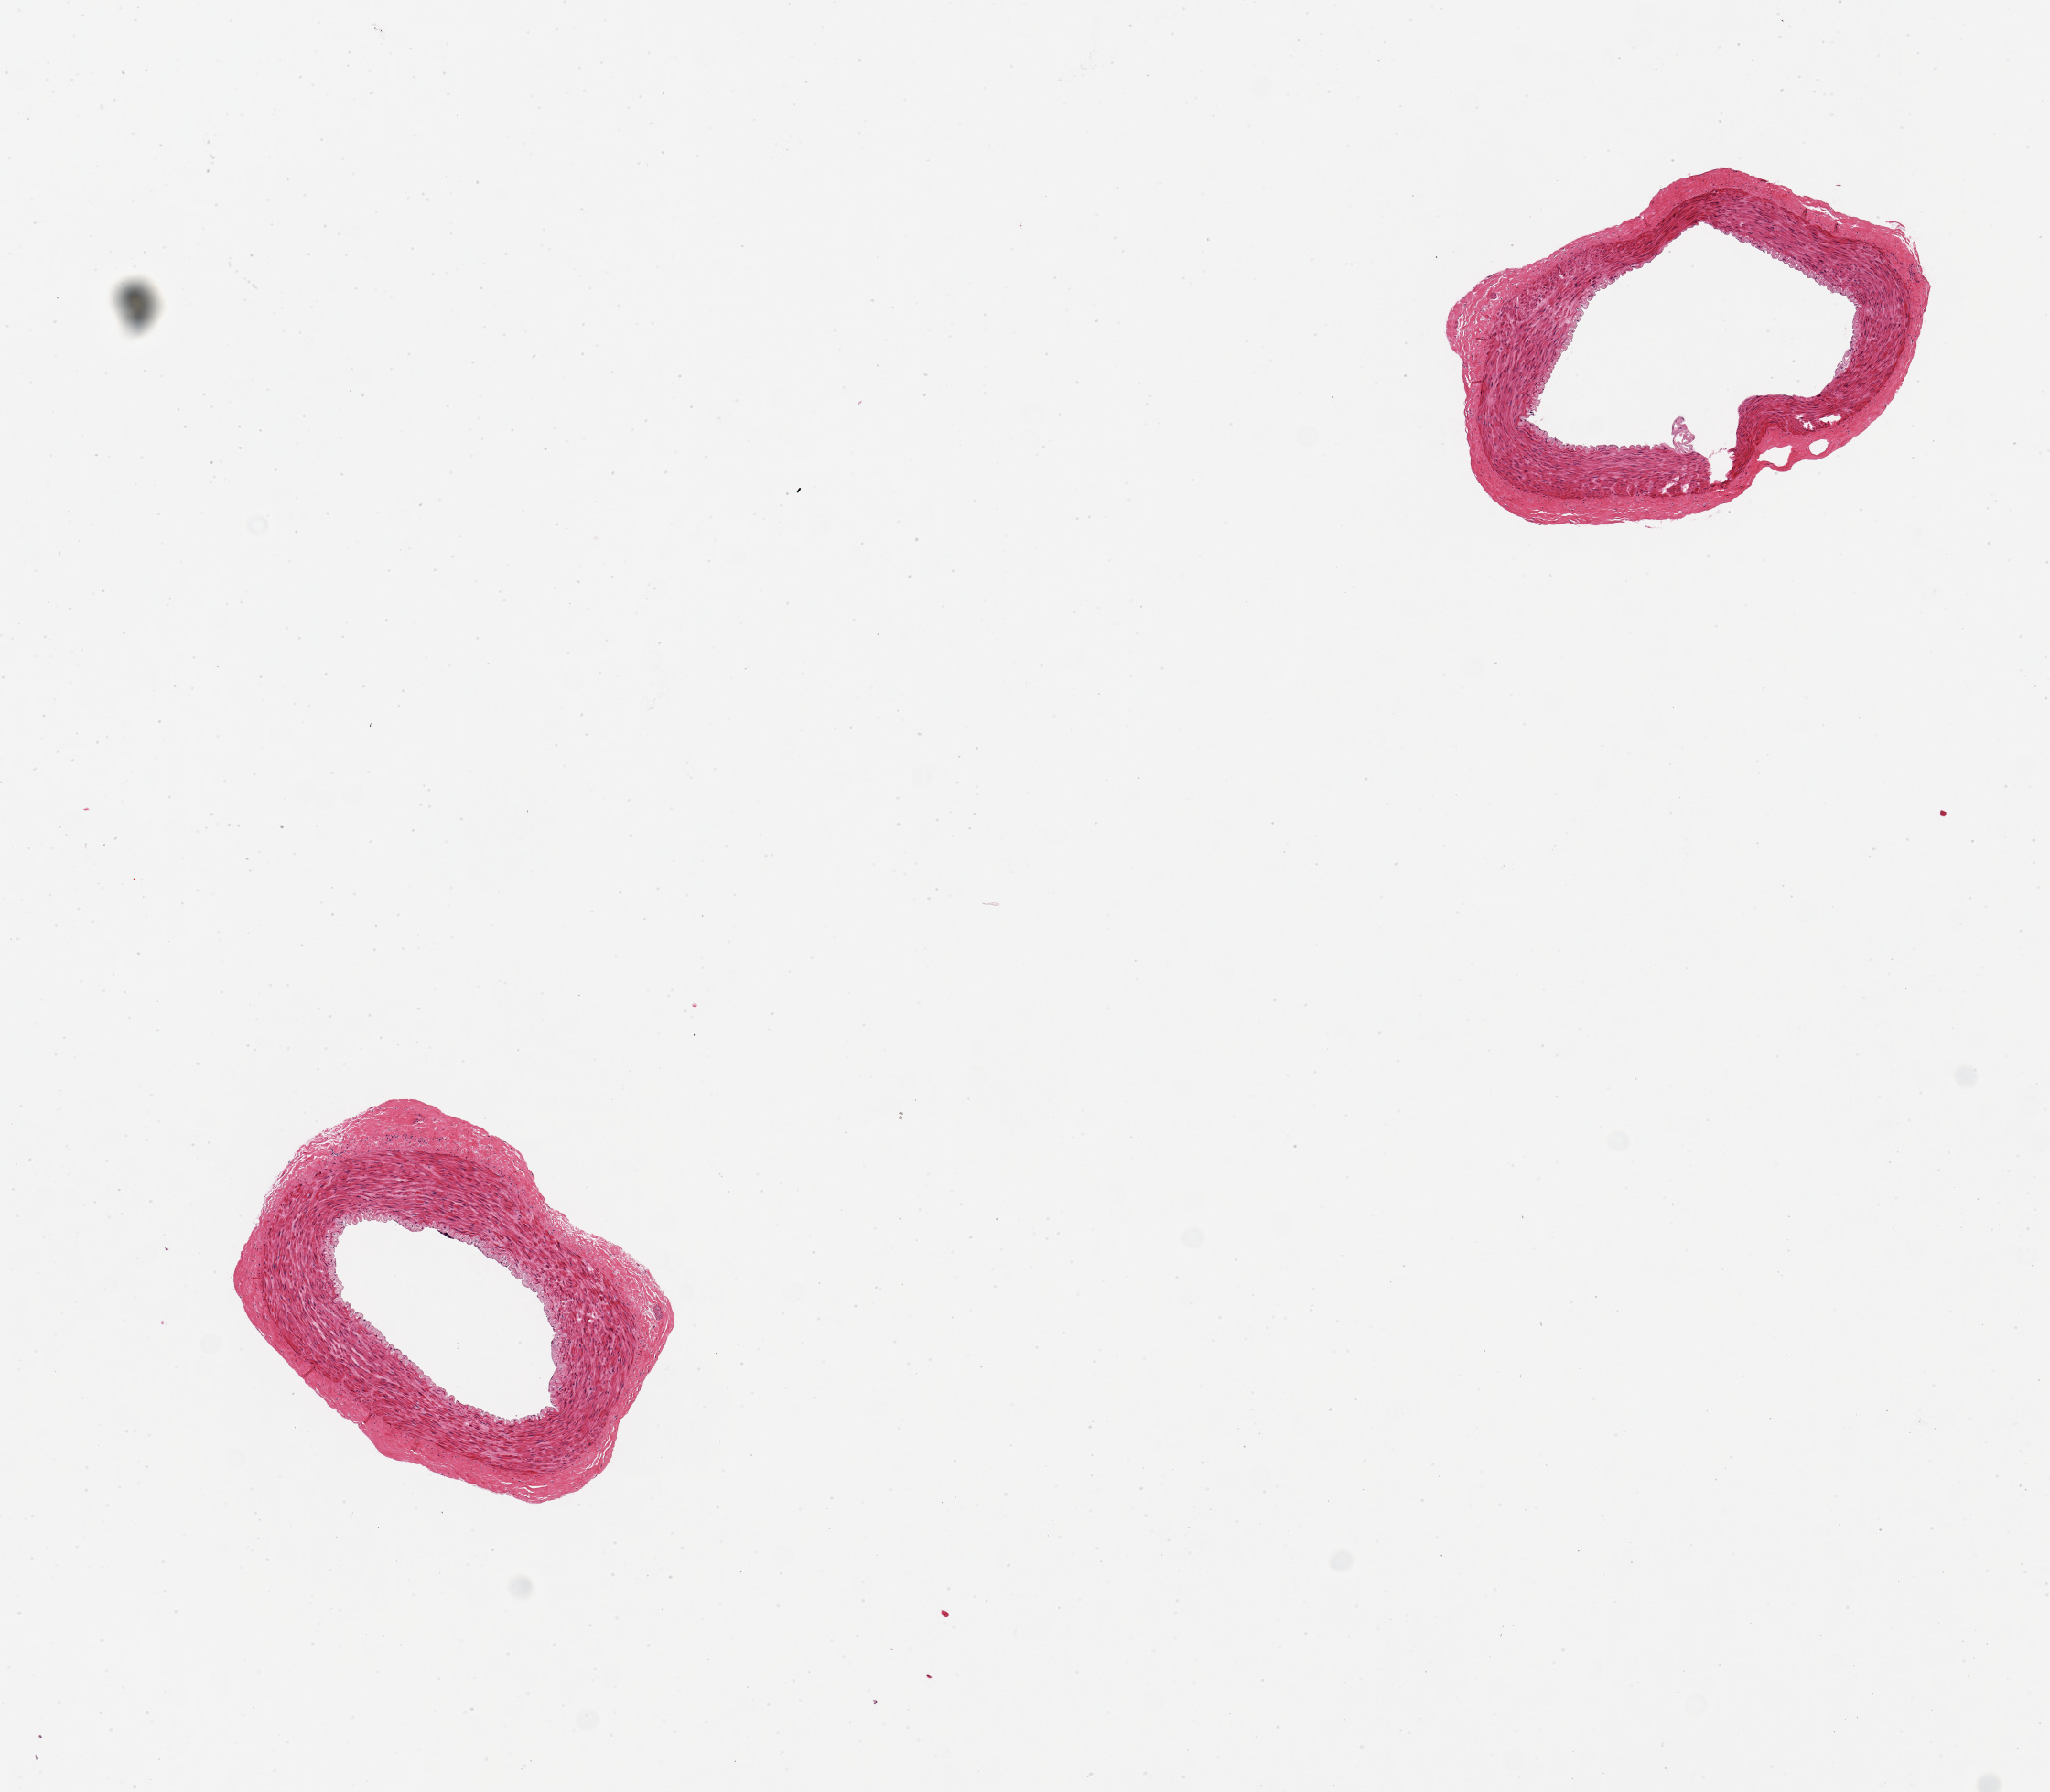
H&E whole-slide image, brightfield — a low-resolution overview of the entire scanned area, about 8.9 x 7.7 mm (from a 20x scan), PAXgene-fixed paraffin-embedded (PFPE) section, target tissue: tibial artery, donor tissue sample. Male donor.
- reviewer comment on this tissue sample: 2 pieces; no lesions; well trimmed of extraneous tissue